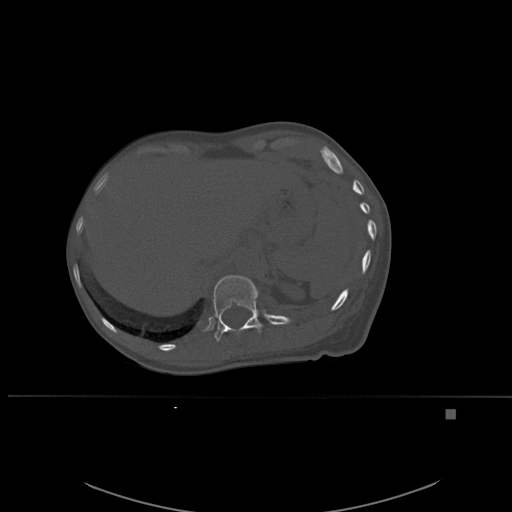
CT including the spine, one axial slice; position 282 of 537 along the scan axis; bone window (W 1800 / L 400 HU); 512 × 512 image matrix, field of view 440 × 440 mm. Patient: female, 45 years. Case-level facts recorded for this patient, not image findings: primary cancer: lung.
Outlined on this slice (semi-automatically segmented with operator editing):
- T12 vertebra: bounding box [x1, y1, x2, y2] px = [213, 275, 262, 342]